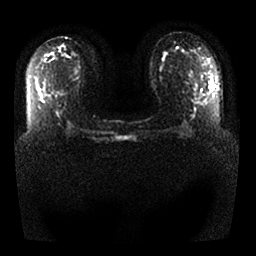
Breast MRI, one axial slice. Slice 15 of 25 in the series (ordered by position). Diffusion-weighted series; image 2 of 4 stored at this slice position (different b-values; order by instance number). 1.5 T. 4 mm slice thickness. 256 × 256 image matrix, field of view 340 × 340 mm. Female patient.
Structures marked on this image (manually delineated by an expert):
- tumour on diffusion-weighted imaging: bounding box [x1, y1, x2, y2] px = [211, 81, 214, 90]